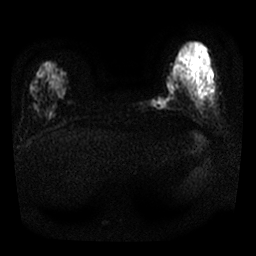
Breast MRI, one axial slice; slice 6 of 25 in the series (ordered by position); diffusion-weighted series; image 2 of 4 stored at this slice position (different b-values; order by instance number); 1.5 T; 4 mm slice thickness; 256 × 256 image matrix. Female patient.
Outlined on this slice (outlined manually by an expert reader):
- tumour on diffusion-weighted imaging: box from (x=153, y=77) to (x=174, y=109) px